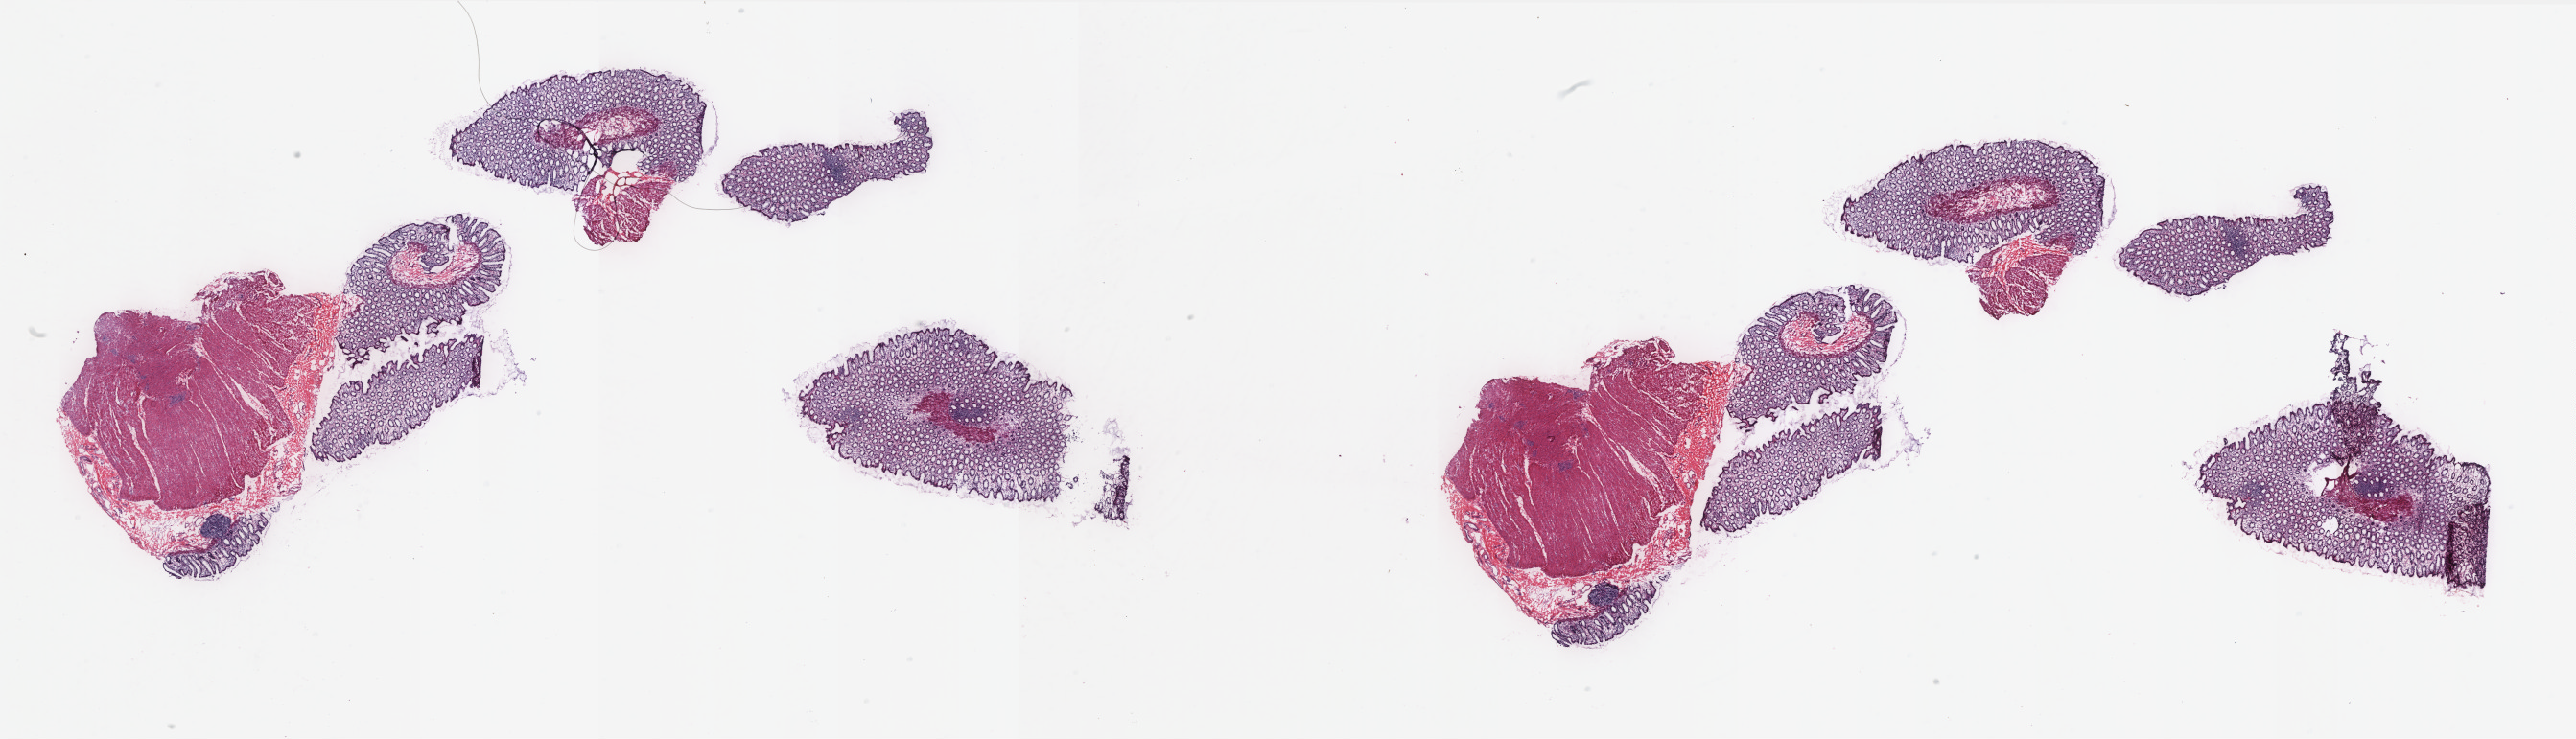
Hematoxylin and eosin (H&E) stained whole-slide image, a low-resolution overview of the entire scanned area, about 42.9 x 12.3 mm (slide scanned at 20x). Frozen section from the top of the tissue portion. Sample: solid tissue normal (non-tumour tissue), rectum. Female patient; age at initial diagnosis 49 years. Slide review estimates, as recorded: tumour cells 0%, normal cells 100%. Inflammatory infiltration, as recorded: lymphocyte infiltration 40%, monocyte infiltration 7%, neutrophil infiltration 0%.
This section: solid tissue normal sample (biorepository sample class). Patient diagnosis: Adenocarcinoma, NOS.